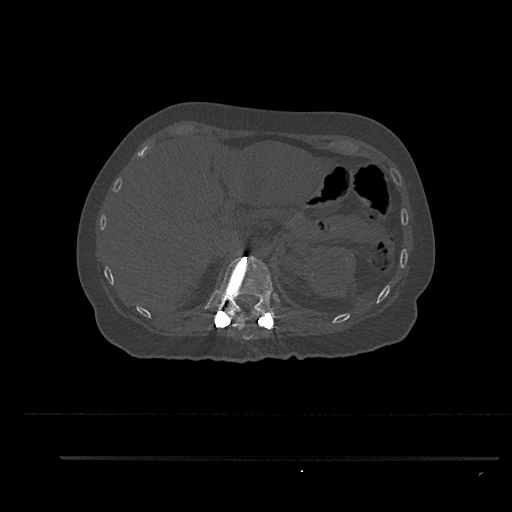
CT including the spine, one axial slice; reconstruction kernel Br40s/3; 120 kVp; bone window (W 1800 / L 400 HU); 512 × 512 image matrix, field of view 408 × 408 mm. Female patient, age 44 years. From the clinical record (not read from this slice): primary cancer: renal; vertebrae with lytic lesions (as recorded): L1.
Outlined on this slice (semi-automatically segmented with operator editing):
- T11 vertebra: bounding box (x1, y1, x2, y2) in pixels: (232, 312, 255, 340)
- T12 vertebra: (215, 249, 282, 328)